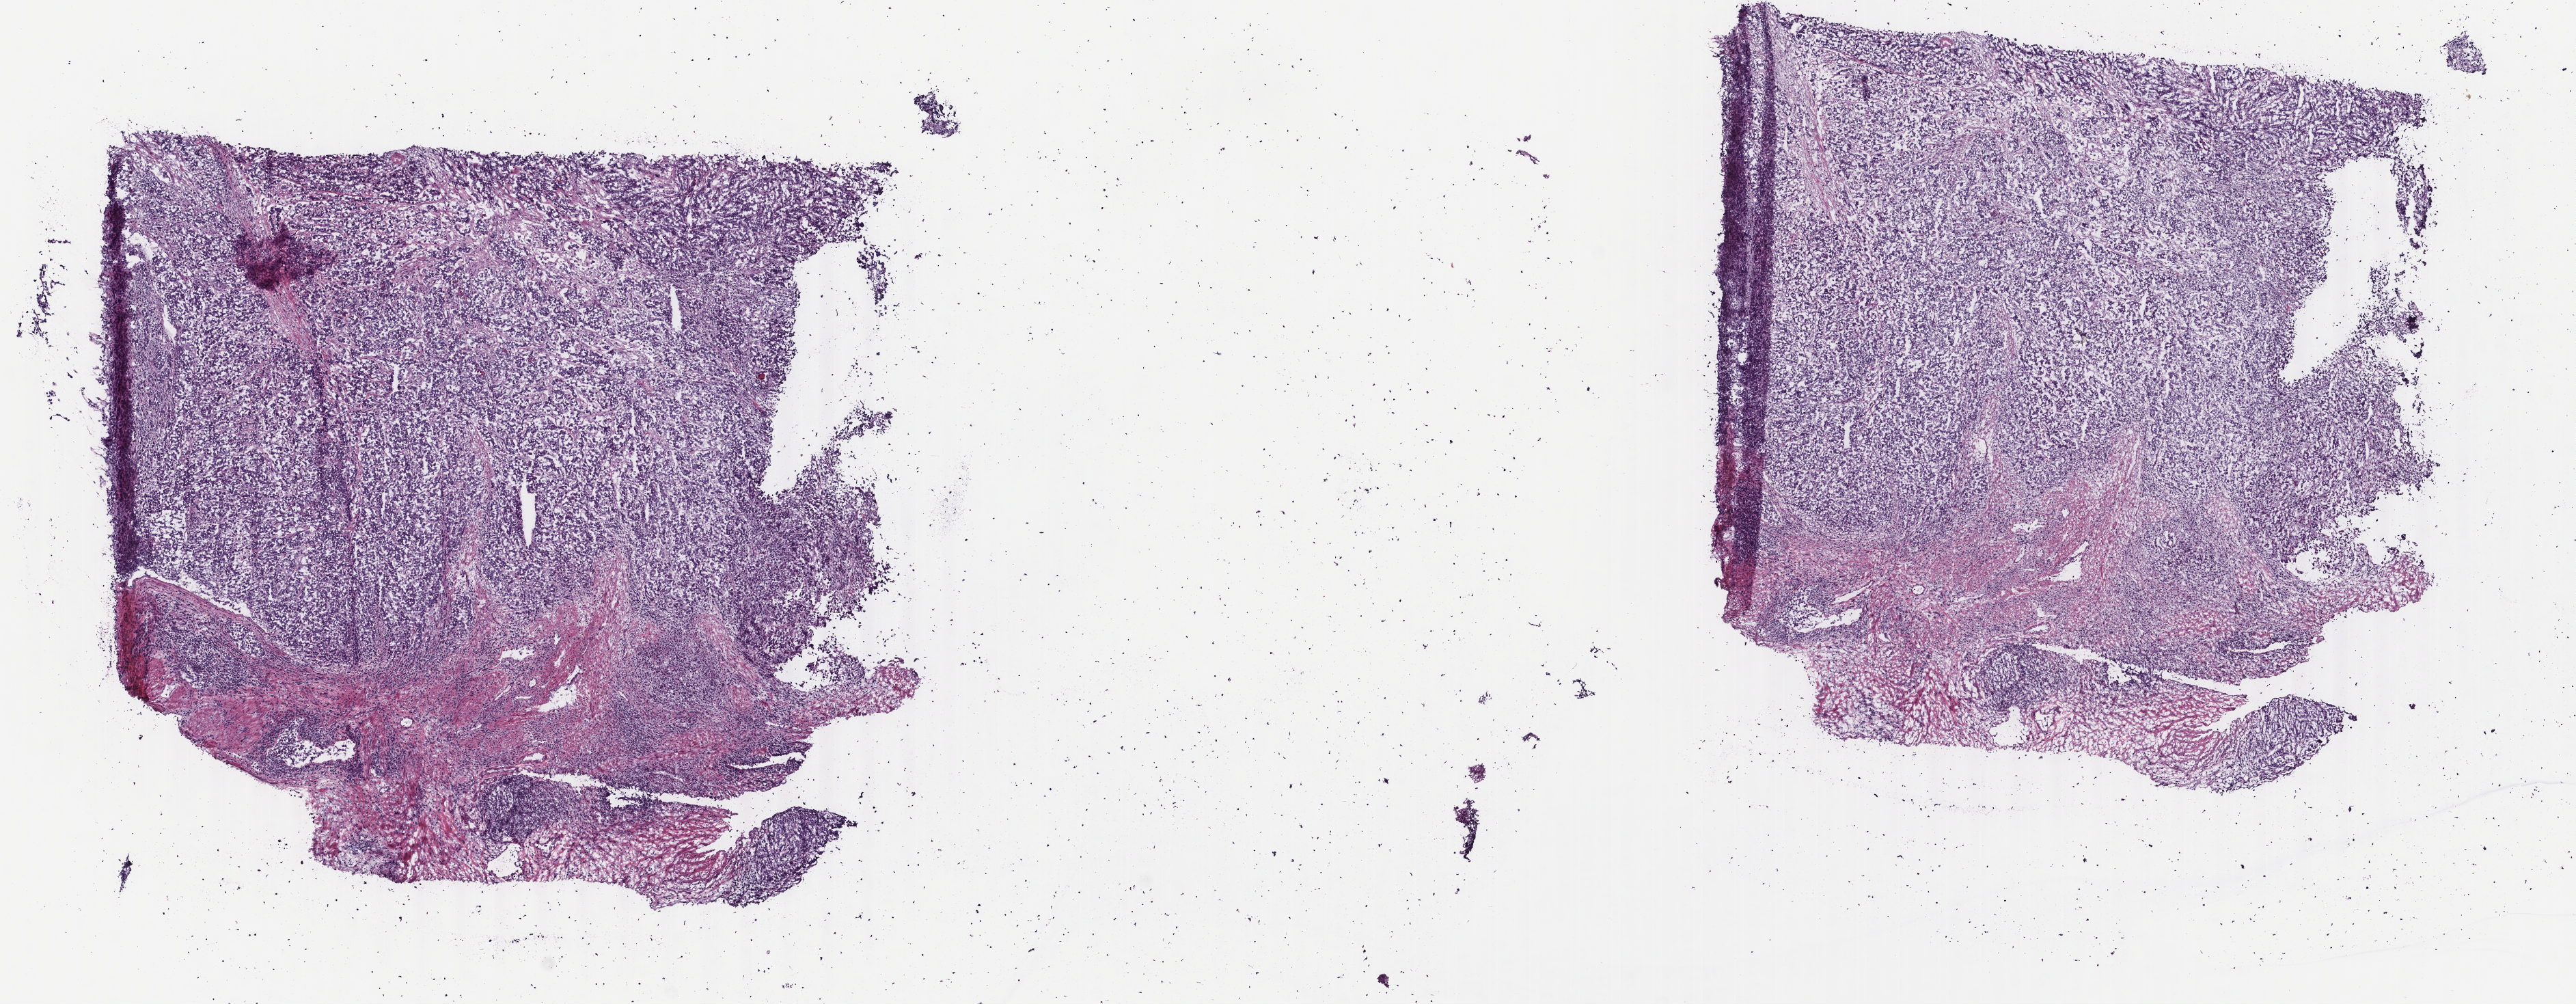
H&E whole-slide image — shown as a low-resolution overview of the whole scanned area (about 15.0 x 5.8 mm), frozen section from the top of the tissue portion, primary tumour sample from the uterus. Female, age 66 years at initial diagnosis. Histologic grade: G3 (poorly differentiated). Composition of this section per pathologist review: tumour cells 70%, tumour nuclei 80%, normal cells 20%, stromal cells 0%, necrosis 10%. Inflammatory infiltration, as recorded: lymphocyte infiltration 20%, monocyte infiltration 0%, neutrophil infiltration 10%.
Histologic diagnosis: Carcinoma, undifferentiated, NOS (endometrium). FIGO stage: IIIC2.